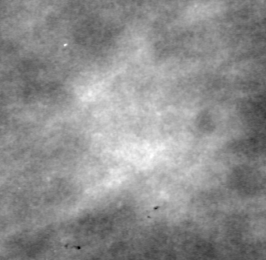
Region of interest cut from a scanned film mammogram (one marked finding), left breast, MLO view.
- Marked abnormality: mass, shape irregular, margins ill defined; BI-RADS assessment category 4; pathology (as recorded): malignant.